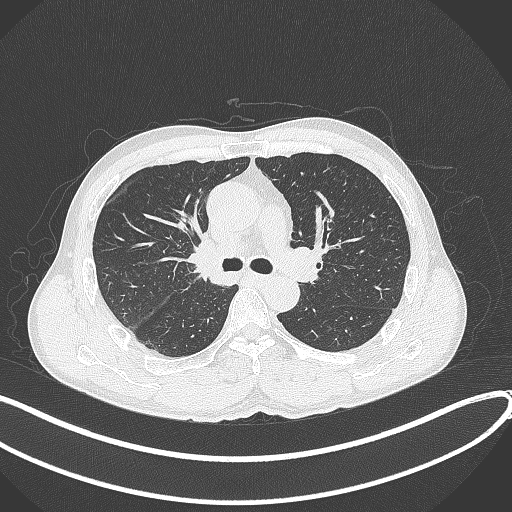
Chest CT, one axial slice. Slice 242 of 409 in the series (ordered by position). Reconstruction kernel B70f. Lung window (W 1500 / L -600 HU). 512 × 512 image matrix, field of view 400 × 400 mm. Male patient, age 53 years. From the clinical record (not read from this slice): clinical TNM (as recorded): T1b N0 M0.
Annotated regions visible in this slice (bounding box drawn by a radiologist):
- lung tumour (recorded histology: squamous cell carcinoma): bounding box (x1, y1, x2, y2) in pixels: (189, 236, 225, 283)